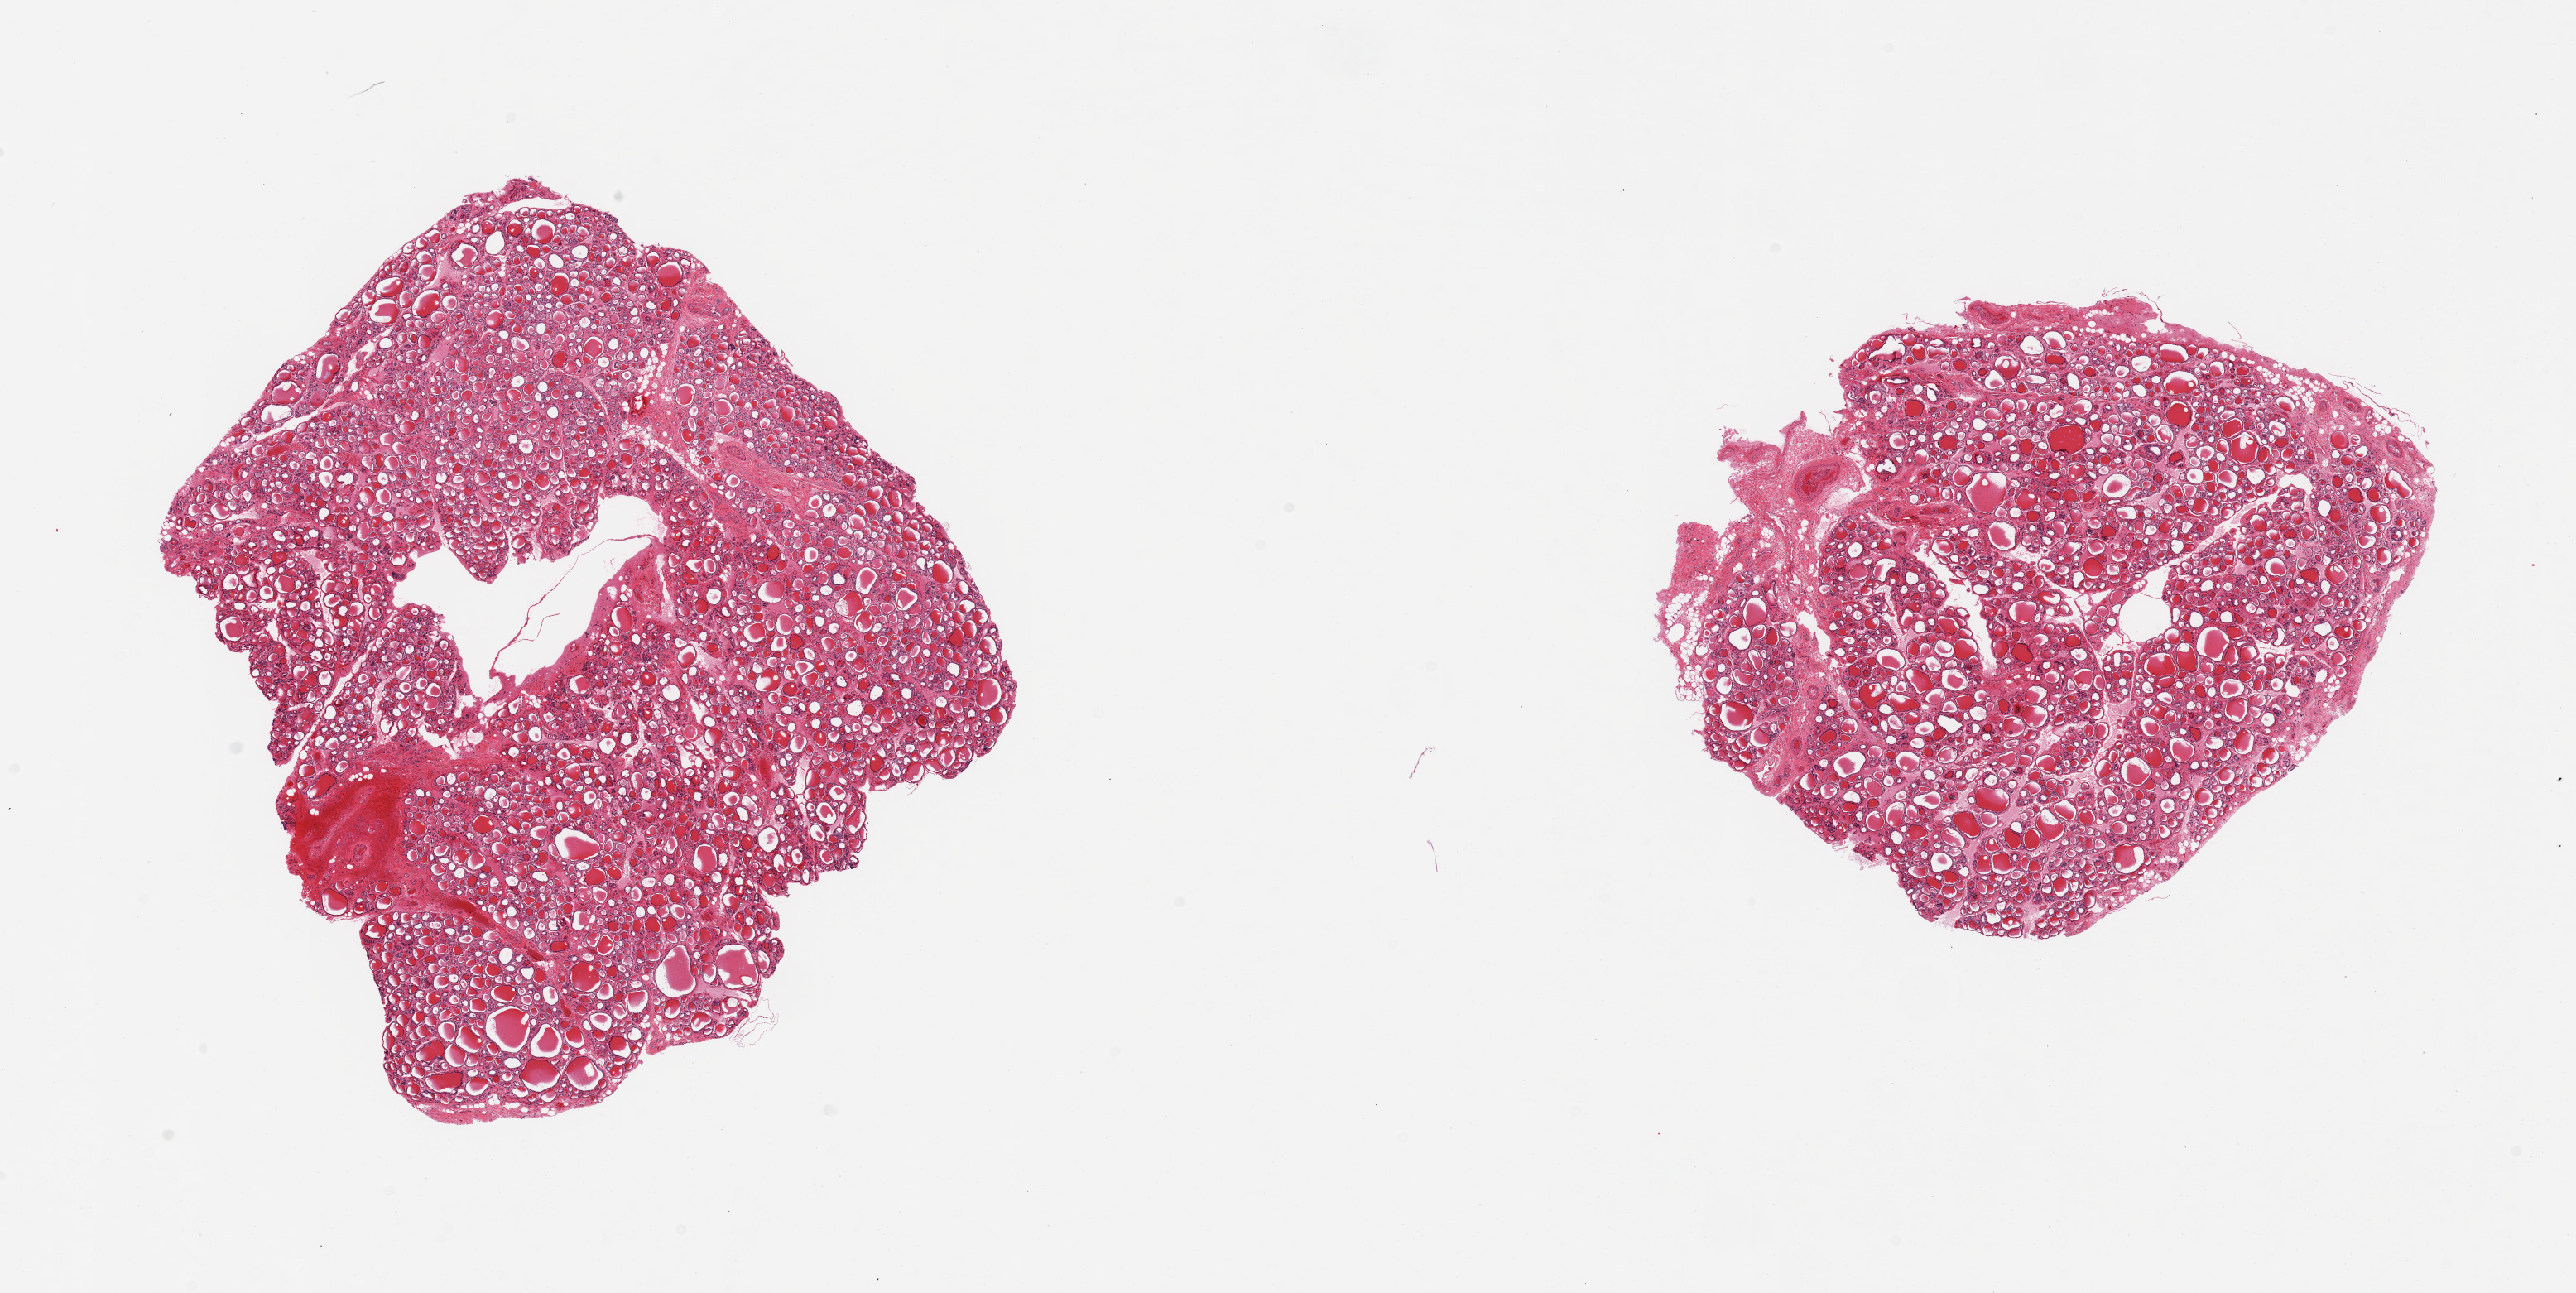
H&E whole-slide image, a low-resolution overview of the entire scanned area, about 24.6 x 12.4 mm (acquisition: 20x scan); PAXgene-fixed paraffin-embedded (PFPE) section; section of thyroid (target tissue); tissue donor sample. Donor sex: female.
Reviewer comment on this tissue sample: 2 pieces, no abornmalities.